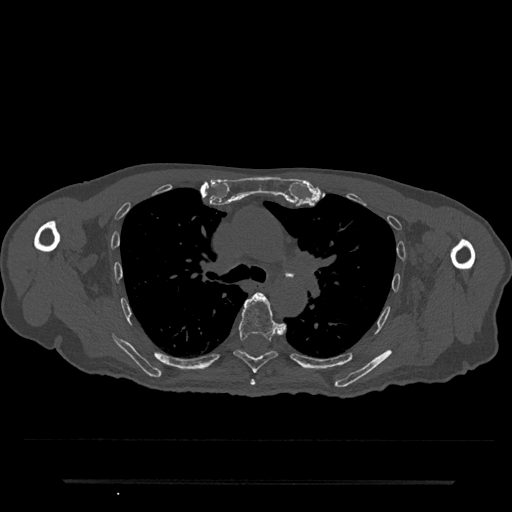
CT including the spine, one axial slice; bone window (W 1800 / L 400 HU); 512 × 512 image matrix. Patient: male, 74 years. From the clinical record (not read from this slice): primary cancer: prostate.
Annotated regions visible in this slice (semi-automatically segmented with operator editing):
- T5 vertebra: bounding box <250,380,256,386> (left, top, right, bottom; pixels)
- T6 vertebra: <233,292,283,374>